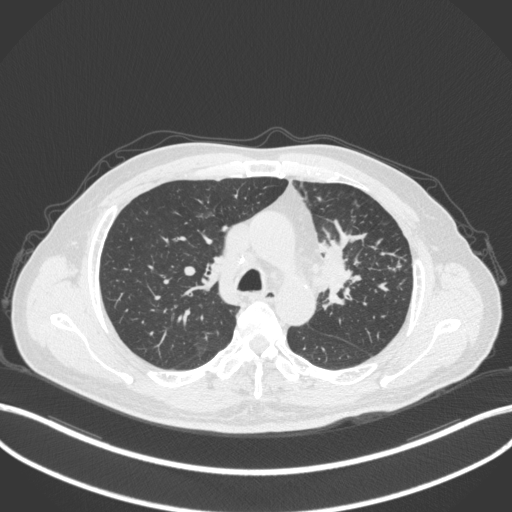
Chest CT, one axial slice; position 238 of 386 along the scan axis; 120 kVp; lung window (W 1500 / L -600 HU); 512 × 512 image matrix. Patient: male, 69 years. From the clinical record (not read from this slice): clinical TNM (as recorded): T2a N2 M0.
Outlined on this slice (rectangle marked by the reading radiologist):
- lung tumour (recorded histology: adenocarcinoma): bounding box <323,233,358,310> (left, top, right, bottom; pixels)